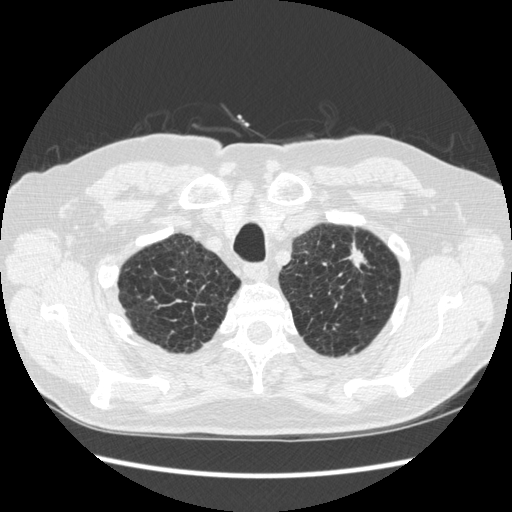
Axial slice from a low-dose chest CT screening exam; third annual screen; lung window (W 1500 / L -600 HU); 1.25 mm slice thickness; standard (soft-tissue) reconstruction kernel (STANDARD); slice 33 of 267 in the series. Male participant, aged 70 years at enrolment. Former smoker at enrolment.
Lesion marked by an expert reader, bounding box <324,231,379,296> (left, top, right, bottom; pixels). The screening reader recorded 2 non-calcified nodules or masses ≥4 mm on this exam (left upper lobe, right lower lobe); which of them this box marks is not recorded. Official screen result: positive, other. Participant outcome: lung cancer diagnosed 92 days after this screen — squamous cell carcinoma, NOS, left upper lobe, moderately differentiated (G2), stage IA (AJCC 6th edition), 18 mm at pathology.